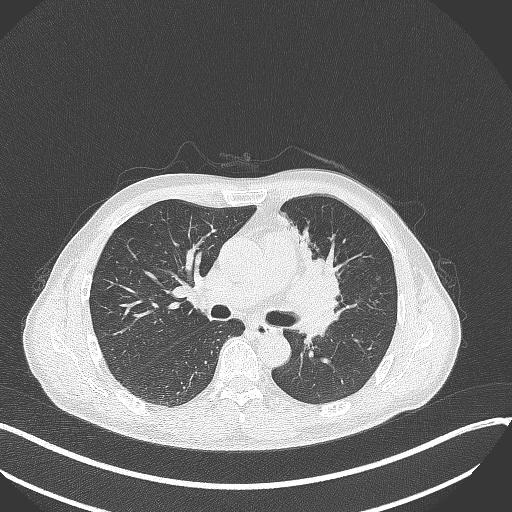
Chest CT, one axial slice; slice 197 of 411 in the series (ordered by position); reconstruction kernel B70f; lung window (W 1500 / L -600 HU); 1 mm slice thickness; 512 × 512 image matrix, field of view 400 × 400 mm. Male patient, age 56 years. Case-level facts recorded for this patient, not image findings: clinical TNM (as recorded): T2a N0 M0.
Outlined on this slice (rectangle marked by the reading radiologist):
- lung tumour (recorded histology: squamous cell carcinoma): bounding box (x1, y1, x2, y2) in pixels: (286, 253, 346, 317)